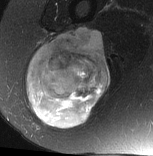
MRI of an extremity soft-tissue mass, one axial slice; position 38 of 77 along the scan axis; T2-weighted fat-saturated; MR volume resampled by the dataset authors to the PET/CT grid (not the native acquisition matrix); 3.27 mm slice thickness; 153 × 156 image matrix. Female patient. From the clinical record (not read from this slice): histological type: synovial sarcoma; grade: intermediate; site of the primary tumour: right buttock.
Outlined on this slice (expert contour drawn on MRI and transferred to this co-registered scan by the dataset authors):
- gross tumour volume including surrounding oedema: bounding box [x1, y1, x2, y2] px = [26, 27, 111, 130]
- gross tumour volume (mass): [26, 27, 111, 130]